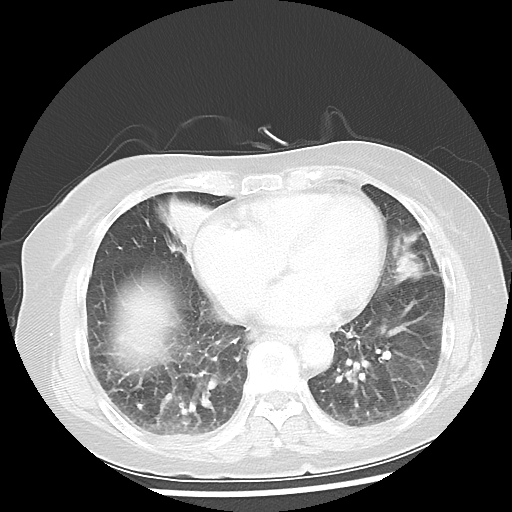
Chest CT, one axial slice; slice 16 of 50 in the series (ordered by position); reconstruction kernel LUNG; lung window (W 1500 / L -600 HU); 5 mm slice thickness; 512 × 512 image matrix, field of view 332 × 332 mm. Patient: female, 77 years. Case-level facts recorded for this patient, not image findings: clinical TNM (as recorded): T2 N3 M1a.
Annotated regions visible in this slice (bounding box drawn by a radiologist):
- lung tumour (recorded histology: adenocarcinoma): box from (x=390, y=231) to (x=427, y=296) px